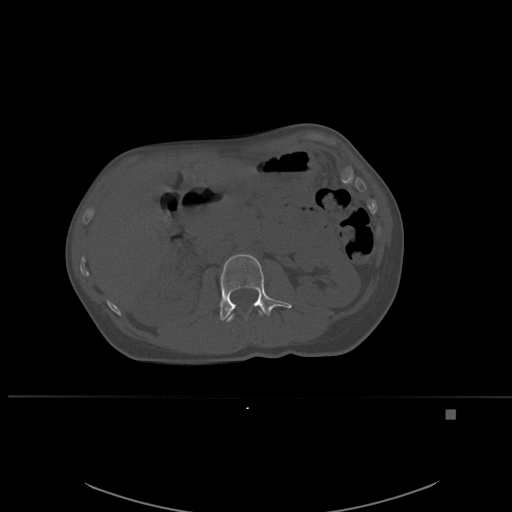
CT including the spine, one axial slice. Position 241 of 537 along the scan axis. Bone window (W 1800 / L 400 HU). 1.5 mm slice thickness. 512 × 512 image matrix. Patient: female, 45 years. Case-level facts recorded for this patient, not image findings: primary cancer: lung.
Structures marked on this image (semi-automatically segmented with operator editing):
- L1 vertebra: bounding box <226,311,264,322> (left, top, right, bottom; pixels)
- L2 vertebra: <219,254,292,321>